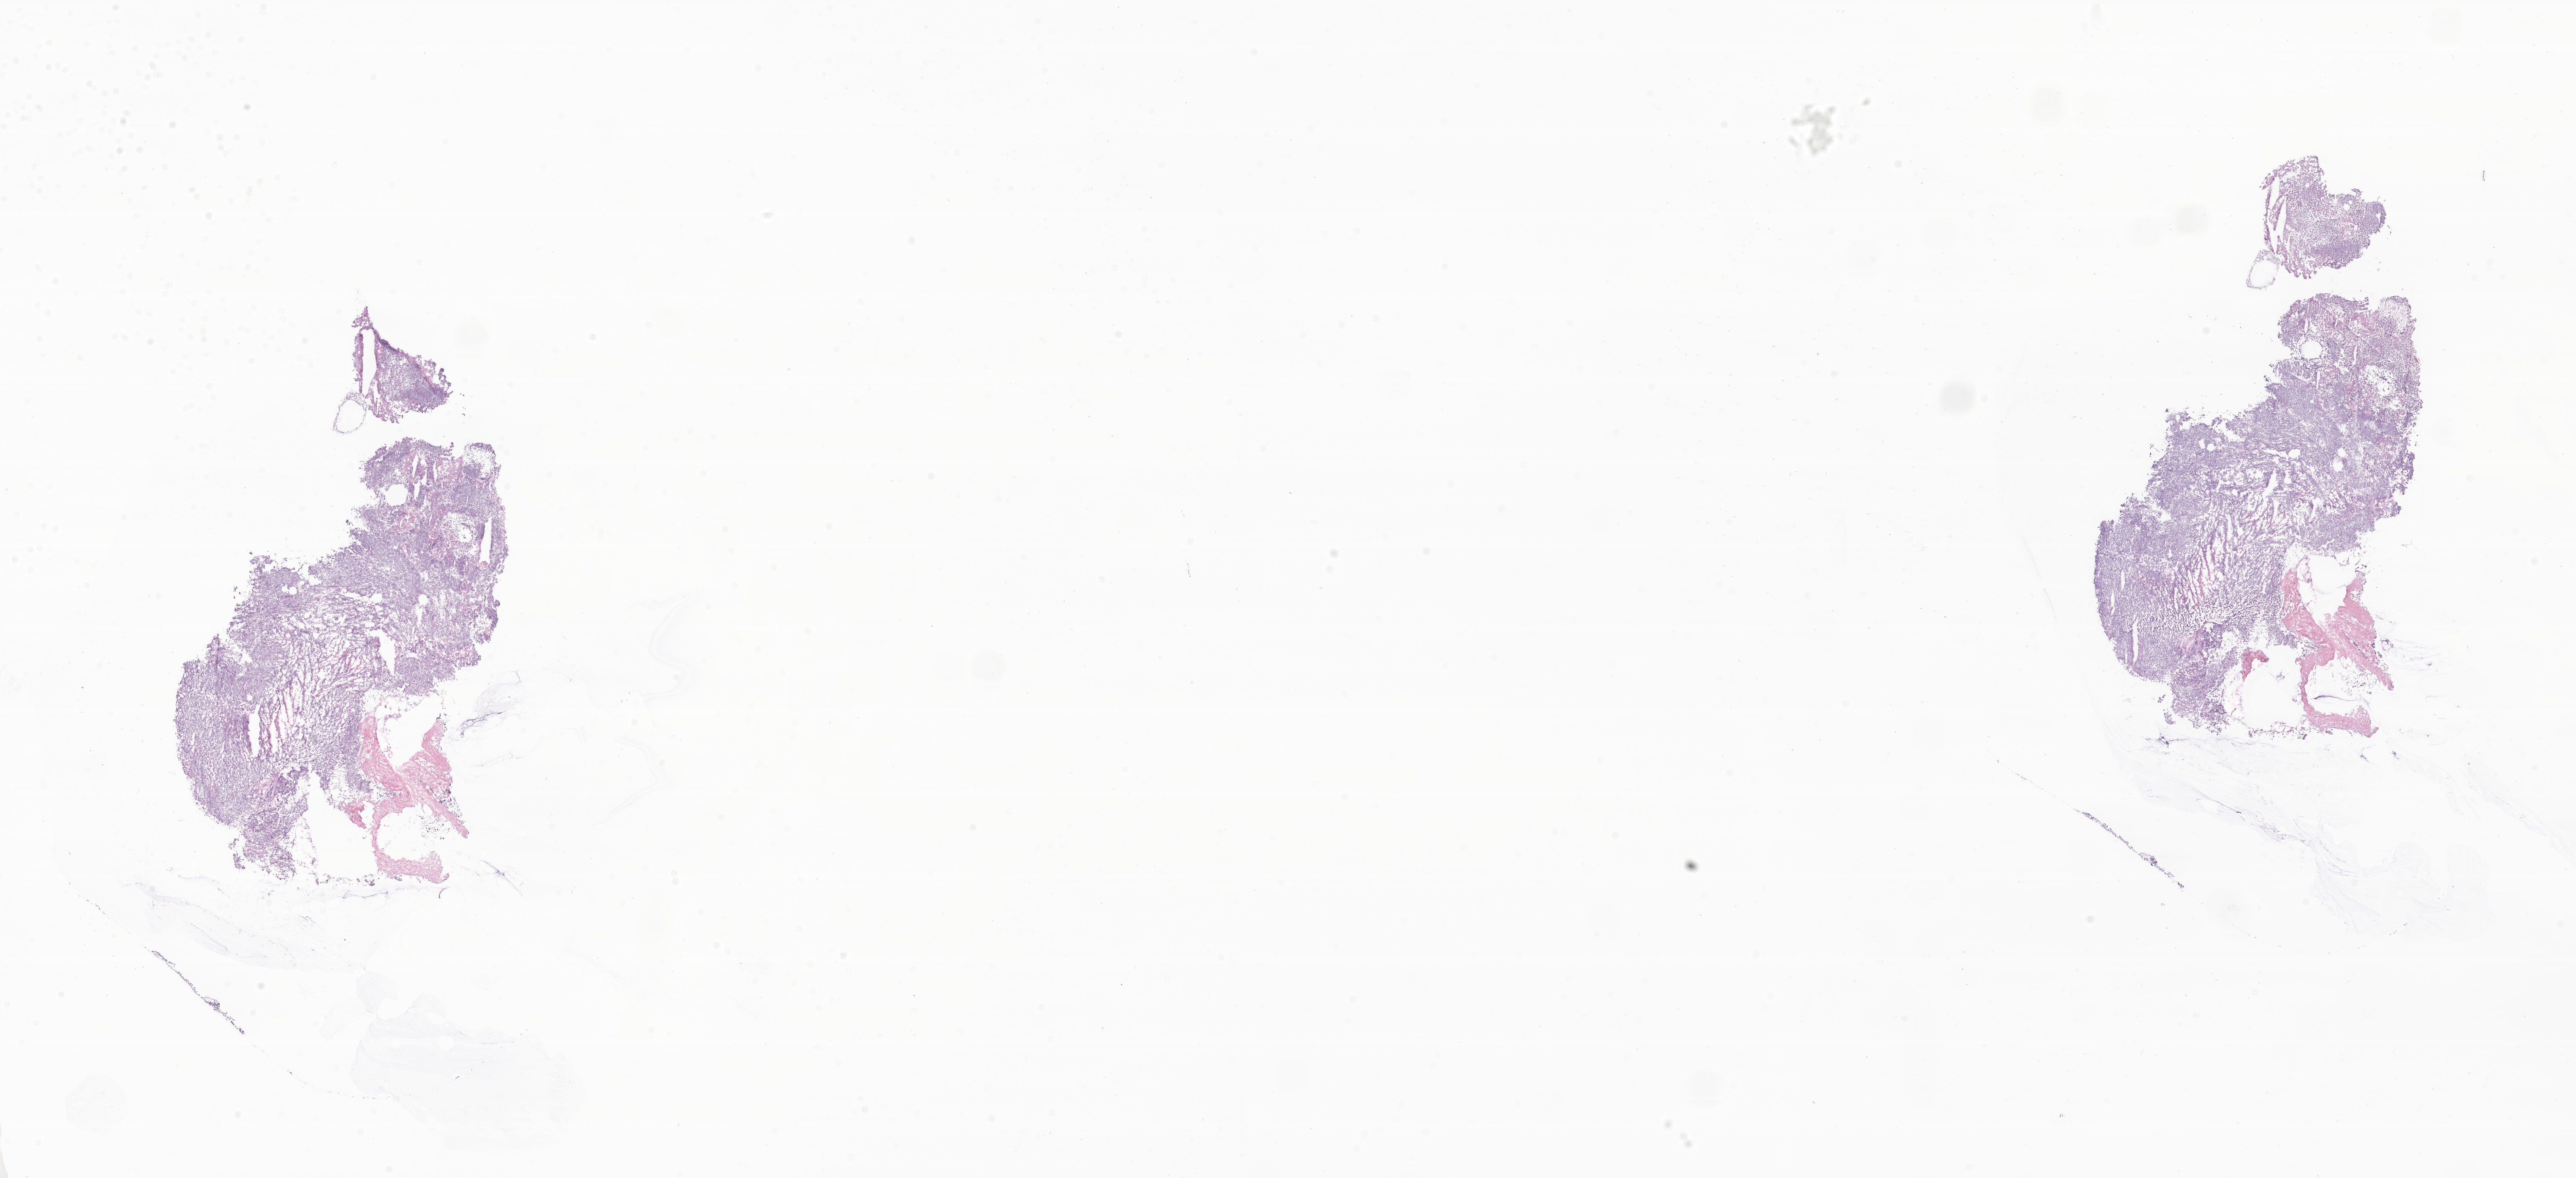
Digitized hematoxylin and eosin (H&E)-stained section of tumor tissue from the soft tissue, shown as a low-resolution overview of the whole scanned area (about 33.2 x 15.2 mm). Frozen section. Patient female; age 351 days.
Diagnosis (ICD-O-3 morphology term): Alveolar rhabdomyosarcoma.